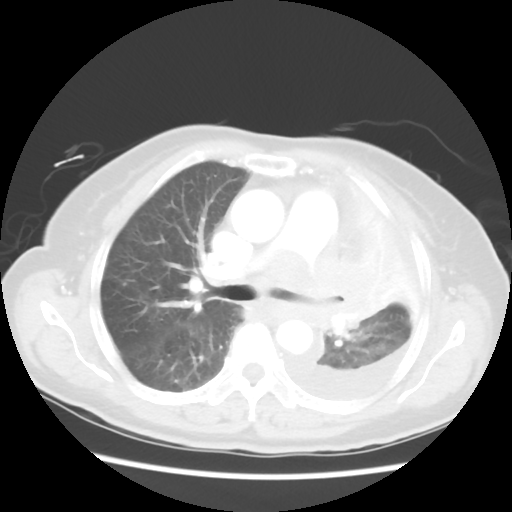
Chest CT, one axial slice. Slice 34 of 52 in the series (ordered by position). 120 kVp. Lung window (W 1500 / L -600 HU). 5 mm slice thickness. 512 × 512 image matrix, field of view 336 × 336 mm. Female patient, age 72 years. From the clinical record (not read from this slice): clinical TNM (as recorded): T4 N3 M1b; histopathological grade: G3.
Structures marked on this image (rectangle marked by the reading radiologist):
- lung tumour (recorded histology: large cell carcinoma): bounding box <298,252,390,339> (left, top, right, bottom; pixels)